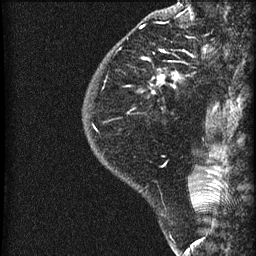
Breast MRI (dynamic contrast-enhanced), one sagittal slice; slice 17 of 60 in the series (ordered by position); dynamic contrast-enhanced series, image 2 of 3 at this slice position (ordered by acquisition); 1.5 T; TE 4.2 ms, TR 22.7 ms; 1.8 mm slice thickness; 256 × 256 image matrix, field of view 180 × 180 mm. Female patient, age 45 years. Case-level facts recorded for this patient, not image findings: setting: breast cancer imaged before/during neoadjuvant chemotherapy; receptor status: HR-positive, HER2-negative.
Annotated regions visible in this slice (semi-automatic segmentation, software-assisted and operator-edited):
- analysis volume of interest (the breast-tissue region the enhancement analysis was run in; not a lesion): bounding box (x1, y1, x2, y2) in pixels: (83, 11, 205, 140)
- tumour enhancement mask (voxels above the 90 % enhancement threshold inside the analysis volume of interest): (149, 50, 166, 81)